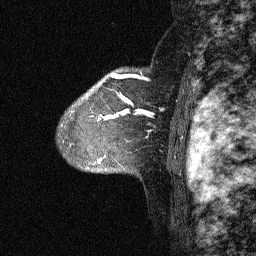
Breast MRI (dynamic contrast-enhanced), one sagittal slice. Slice 48 of 64 in the series (ordered by position). Dynamic contrast-enhanced study with each time point stored as its own series, time point 2 of 3 at this slice position (early post-contrast, ordered by acquisition time). 1.5 T. TE 4.5 ms, TR 11 ms. 256 × 256 image matrix, field of view 200 × 200 mm. Patient: female, 46 years. From the clinical record (not read from this slice): setting: breast cancer imaged before/during neoadjuvant chemotherapy; receptor status: HER2-positive.
Annotated regions visible in this slice (semi-automatic segmentation, software-assisted and operator-edited):
- analysis volume of interest (the breast-tissue region the enhancement analysis was run in; not a lesion): box from (x=44, y=72) to (x=164, y=177) px
- tumour enhancement mask (voxels above the 90 % enhancement threshold inside the analysis volume of interest): (x=99, y=74)–(x=163, y=164)